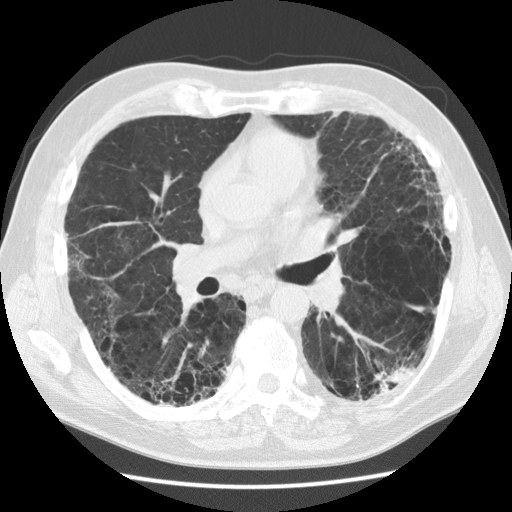
Low-dose screening chest CT, one axial slice; position 67 of 128 along the scan axis; reconstruction kernel STANDARD; lung window (W 1500 / L -600 HU); 2.5 mm slice thickness; 512 × 512 image matrix.
Outlined on this slice (manually delineated by an expert):
- lesion 1 (tumor, lower lobe of left lung): bounding box <387,365,413,384> (left, top, right, bottom; pixels)